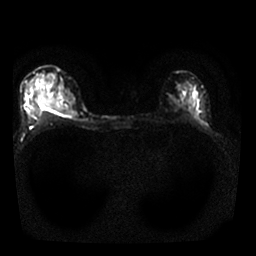
Breast MRI, one axial slice. Slice 16 of 25 in the series (ordered by position). Diffusion-weighted series; image 2 of 4 stored at this slice position (different b-values; order by instance number). 1.5 T. 4 mm slice thickness. 256 × 256 image matrix. Female patient.
Structures marked on this image (expert manual segmentation):
- tumour on diffusion-weighted imaging: bounding box [x1, y1, x2, y2] px = [40, 98, 74, 116]